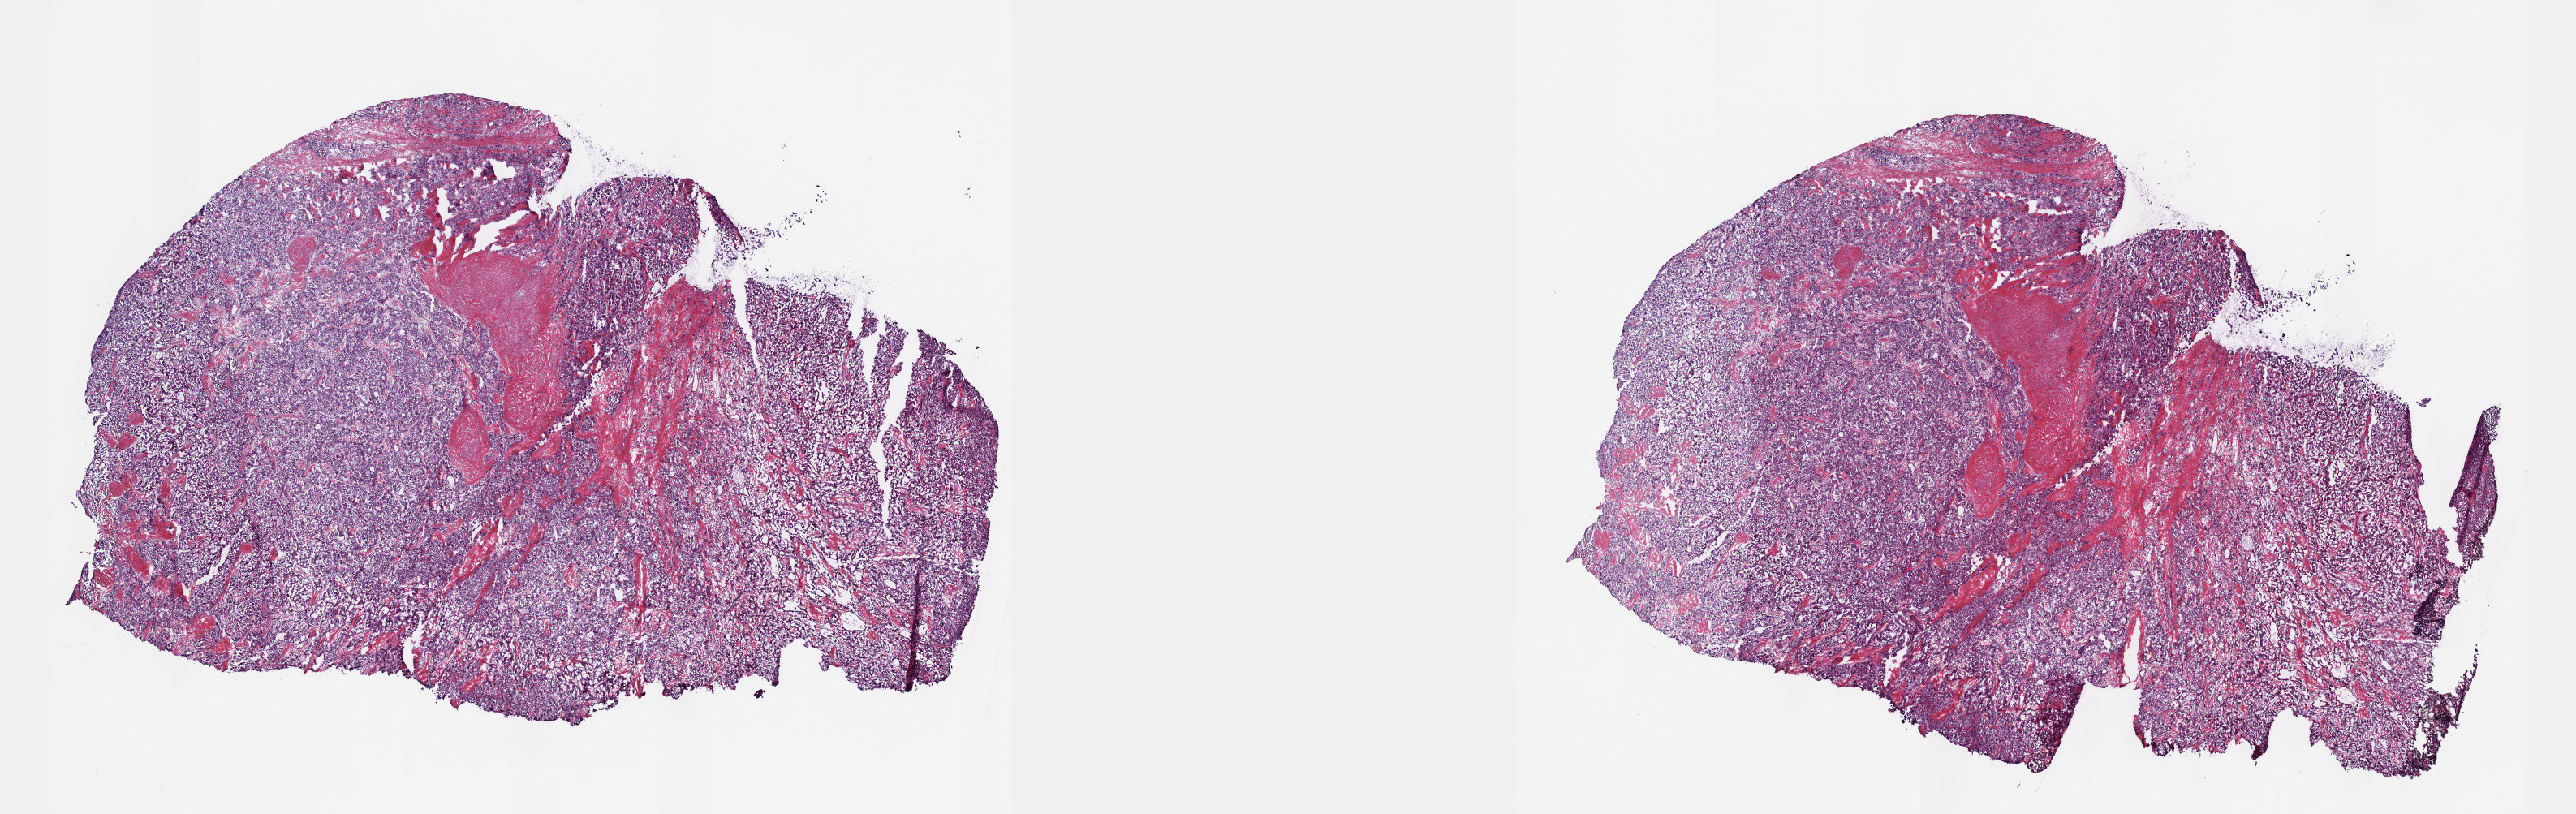
Digitized H&E tissue section (whole slide), a low-resolution overview of the entire scanned area, about 25.7 x 8.1 mm (from a 40x scan). Frozen section from the top of the tissue portion. Sample: primary tumour, liver. Female, age 17 years at initial diagnosis. Histologic grade: G3 (poorly differentiated). Pathologist review of this section (percent, as recorded): tumour cells 80%, tumour nuclei 92%, normal cells 0%, stromal cells 19%, necrosis 1%. Infiltration values recorded for this section: lymphocyte infiltration 3%, monocyte infiltration 0%, neutrophil infiltration 0%.
AJCC pathologic stage: IIIA (7th edition). TNM: T3a N0 M0. Diagnosis: Hepatocellular carcinoma, NOS.